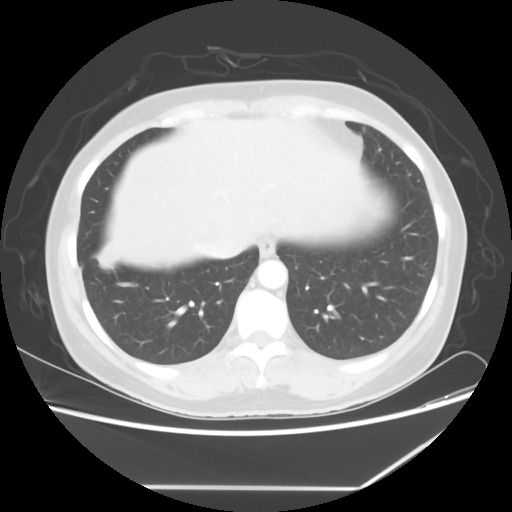
Chest CT, one axial slice. Position 17 of 60 along the scan axis. Reconstruction kernel STANDARD. Lung window (W 1500 / L -600 HU). 5 mm slice thickness. 512 × 512 image matrix. Female patient, age 42 years. Case-level facts recorded for this patient, not image findings: clinical TNM (as recorded): T2 N1 M0.
Outlined on this slice (rectangle marked by the reading radiologist):
- lung tumour (recorded histology: adenocarcinoma): bounding box (x1, y1, x2, y2) in pixels: (95, 239, 125, 271)